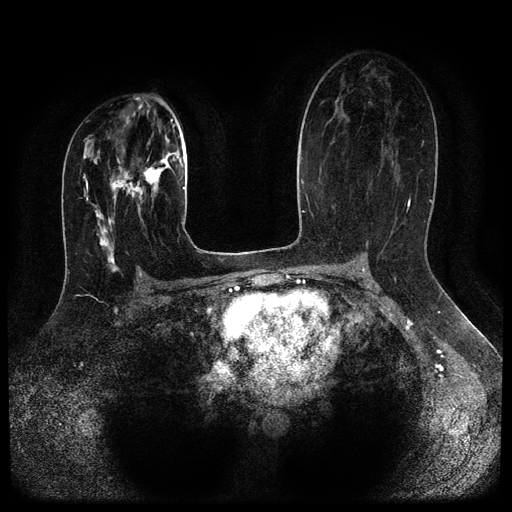
Breast MRI (dynamic contrast-enhanced, multi-phase), one axial slice; slice 60 of 116 in the series (ordered by position); dynamic contrast-enhanced series, time point 2 of 5 at this slice position (early post-contrast); 1.5 T; TE 2.6 ms, TR 5.4 ms; 2 mm slice thickness; 512 × 512 image matrix, field of view 340 × 340 mm. Patient: female, 29 years.
Outlined on this slice (semi-automatic segmentation, software-assisted and operator-edited):
- breast lesion (labelled 'tumour' in the annotation; benign lesions carry a separate 'benign' label): box from (x=109, y=155) to (x=173, y=211) px
- breast lesion (labelled benign in the annotation): (x=93, y=205)–(x=117, y=273)